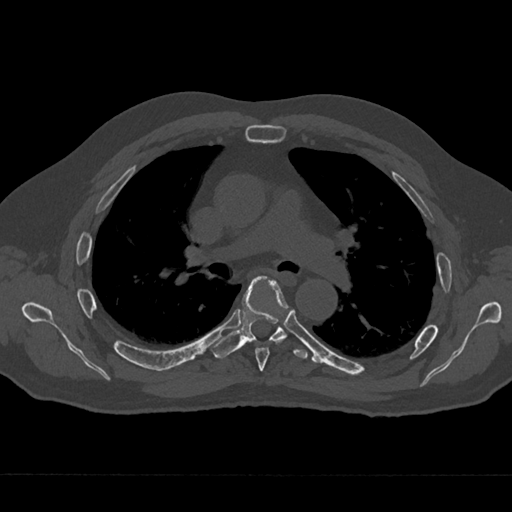
CT including the spine, one axial slice. Slice 447 of 797 in the series (ordered by position). Reconstruction kernel Br40s/3. 120 kVp. Bone window (W 1800 / L 400 HU). 0.5 mm slice thickness. 512 × 512 image matrix, field of view 377 × 377 mm. Patient: male, 75 years. From the clinical record (not read from this slice): primary cancer: renal; vertebrae with lytic lesions (as recorded): T4.
Outlined on this slice (semi-automatically segmented with operator editing):
- T5 vertebra: bounding box (x1, y1, x2, y2) in pixels: (255, 280, 289, 371)
- T6 vertebra: (210, 276, 308, 359)